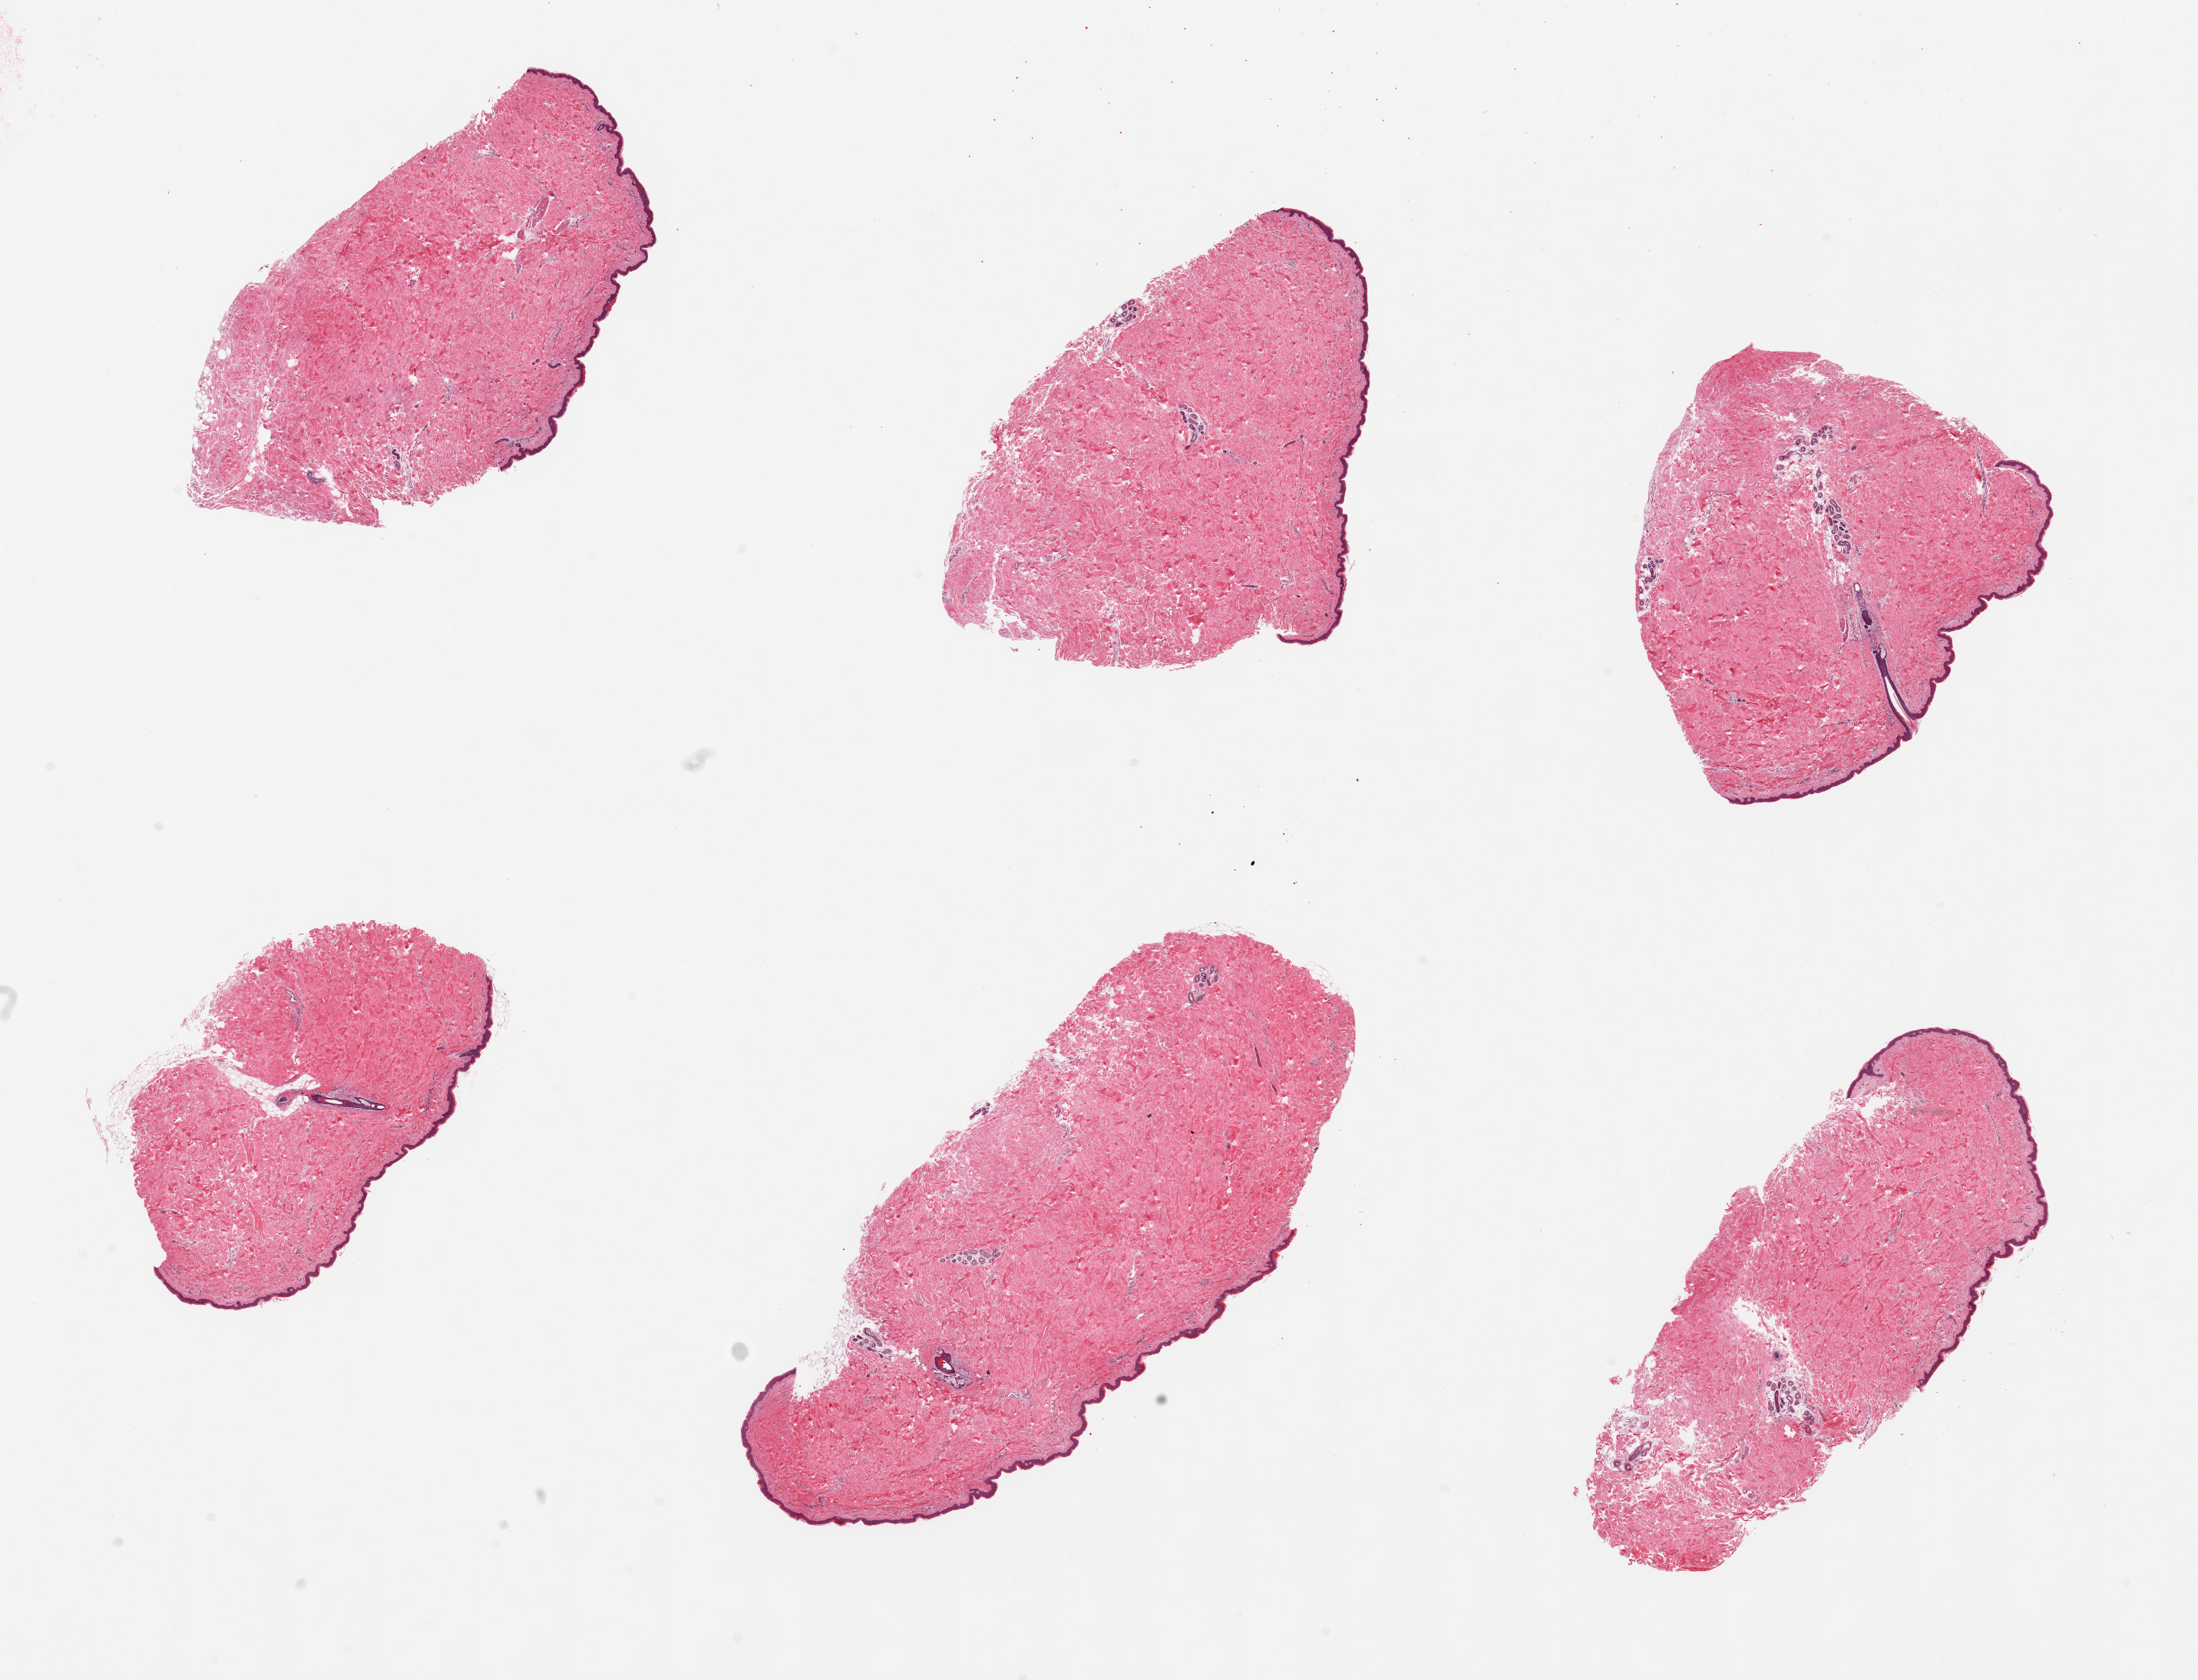
Digitized hematoxylin and eosin (H&E)-stained section, brightfield, low-resolution overview of the scanned area, about 22.6 x 17.3 mm, PAXgene-fixed paraffin-embedded (PFPE) section, sampled site (target tissue): skin of suprapubic region, tissue donor sample.
• review note (as recorded): 6 pieces; well trimmed; minimal dermal fat